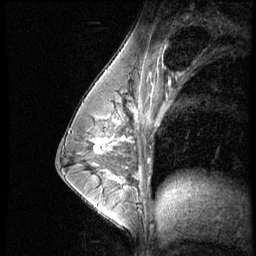
Breast MRI (dynamic contrast-enhanced), one sagittal slice. Position 33 of 56 along the scan axis. Dynamic contrast-enhanced series, image 2 of 4 at this slice position (ordered by acquisition). 1.5 T. TE 4.2 ms, TR 8.9 ms. 2.5 mm slice thickness. 256 × 256 image matrix. Patient: female, 35 years. Case-level facts recorded for this patient, not image findings: setting: breast cancer imaged before/during neoadjuvant chemotherapy; receptor status: HER2-positive.
Structures marked on this image (semi-automatic segmentation, software-assisted and operator-edited):
- analysis volume of interest (the breast-tissue region the enhancement analysis was run in; not a lesion): bounding box (x1, y1, x2, y2) in pixels: (73, 111, 131, 164)
- tumour enhancement mask (voxels above the 140 % enhancement threshold inside the analysis volume of interest): (95, 118, 126, 154)